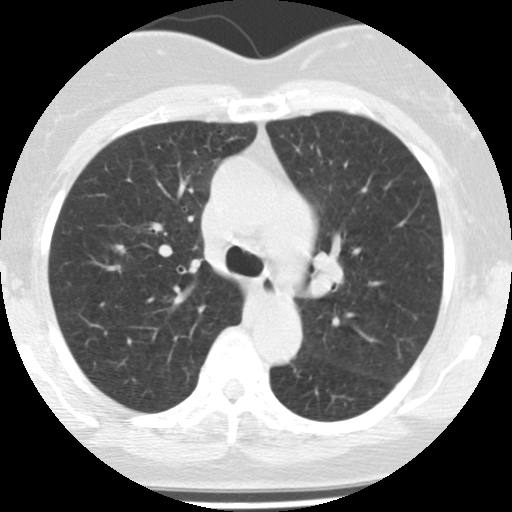
Axial slice from a low-dose chest CT screening exam. Baseline screening round. Lung window (W 1500 / L -600 HU). Standard (soft-tissue) reconstruction kernel (STANDARD). Female participant, aged 62 years at enrolment.
Lesion marked by an expert reader, bounding box <93,227,141,275> (left, top, right, bottom; pixels). Screening reader's record for this exam: no non-calcified nodule ≥4 mm recorded. Participant outcome: lung cancer diagnosed 865 days after this screen (after the third annual screen) — adenocarcinoma, NOS, right upper lobe, well differentiated (G1), stage IA (AJCC 6th edition), 7 mm at pathology.